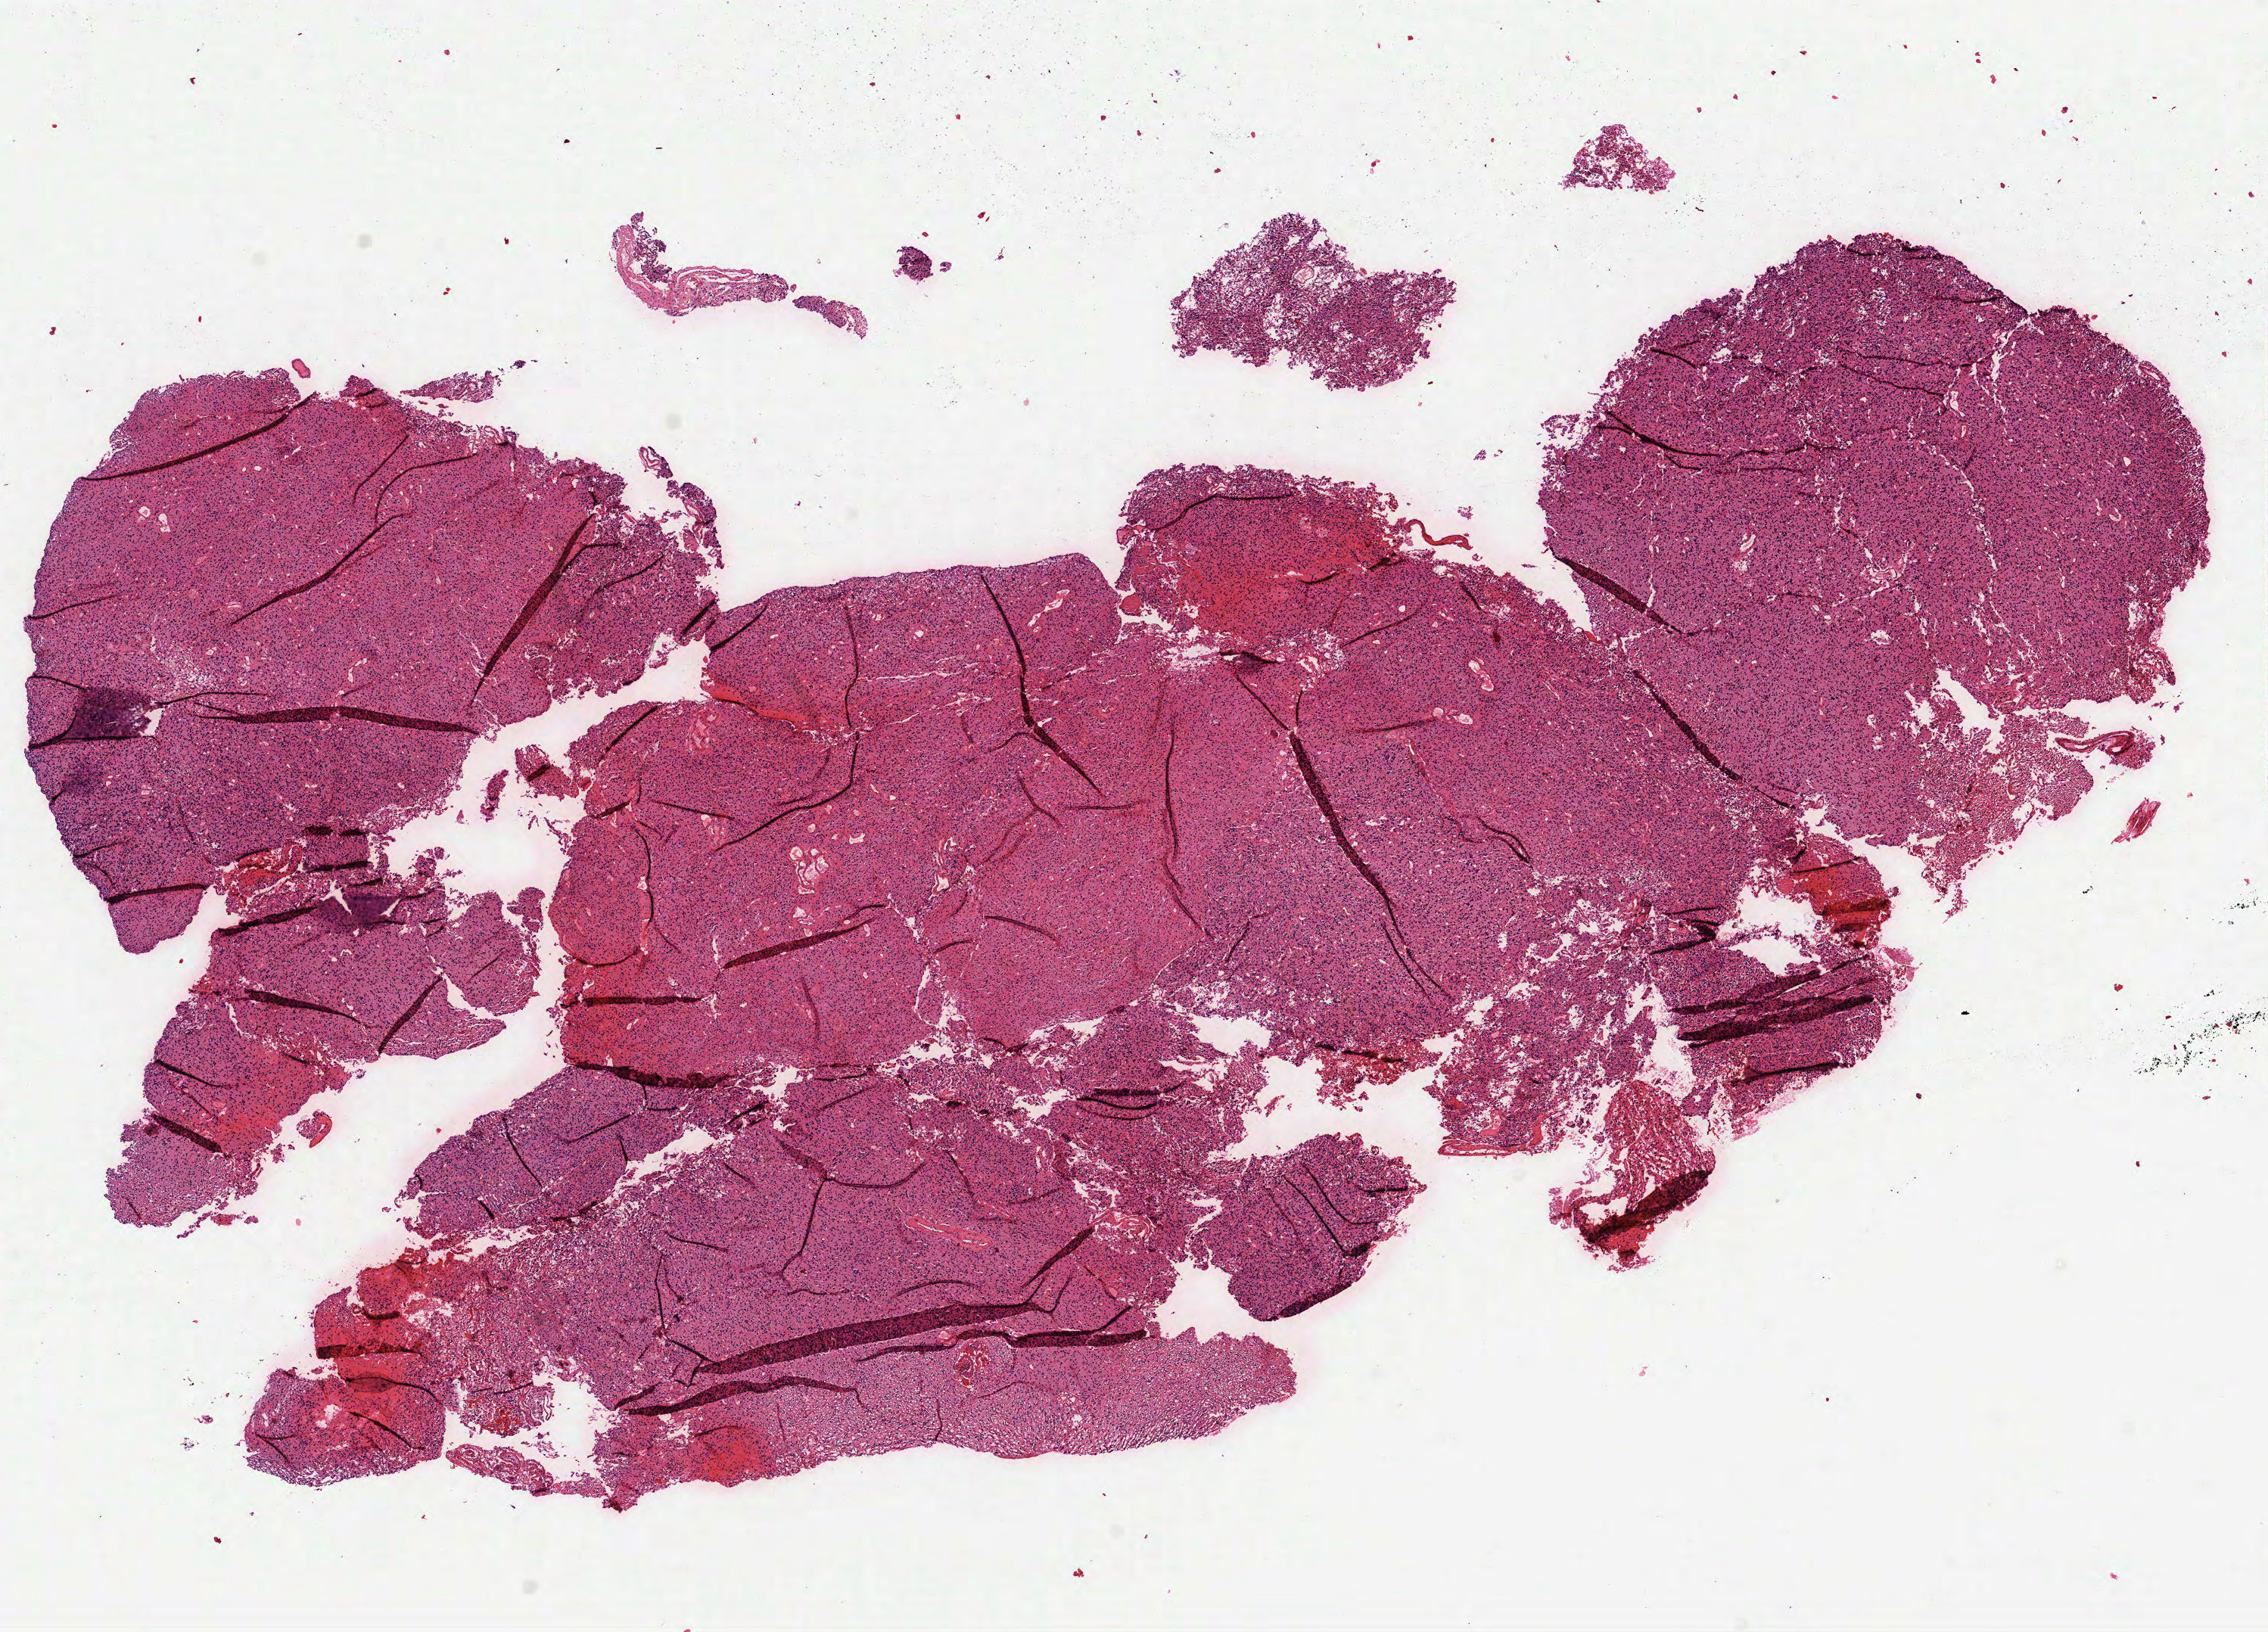
Hematoxylin and eosin (H&E) stained whole-slide image, whole scanned area (about 12.1 x 8.7 mm) shown as a low-resolution overview, formalin-fixed paraffin-embedded (FFPE) diagnostic section, brain, primary tumour sample. Female, age 39 years at initial diagnosis. Histologic grade: G2 (moderately differentiated).
Diagnosis: Astrocytoma, NOS.